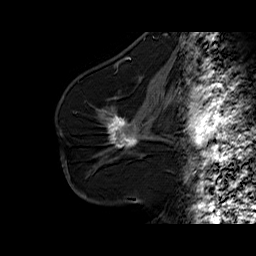
Breast MRI (dynamic contrast-enhanced), one sagittal slice. Position 34 of 60 along the scan axis. Dynamic contrast-enhanced series, time point 2 of 6 at this slice position (early post-contrast). 1.5 T. TE 6.3 ms, TR 32.5 ms. 256 × 256 image matrix, field of view 200 × 200 mm. Female patient. From the clinical record (not read from this slice): setting: breast cancer imaged before/during neoadjuvant chemotherapy; receptor status: HR-positive, HER2-negative.
Outlined on this slice (semi-automatically segmented with operator editing):
- analysis volume of interest (the breast-tissue region the enhancement analysis was run in; not a lesion): bounding box <95,103,161,164> (left, top, right, bottom; pixels)
- tumour enhancement mask (voxels above the 100 % enhancement threshold inside the analysis volume of interest): <107,115,138,147>